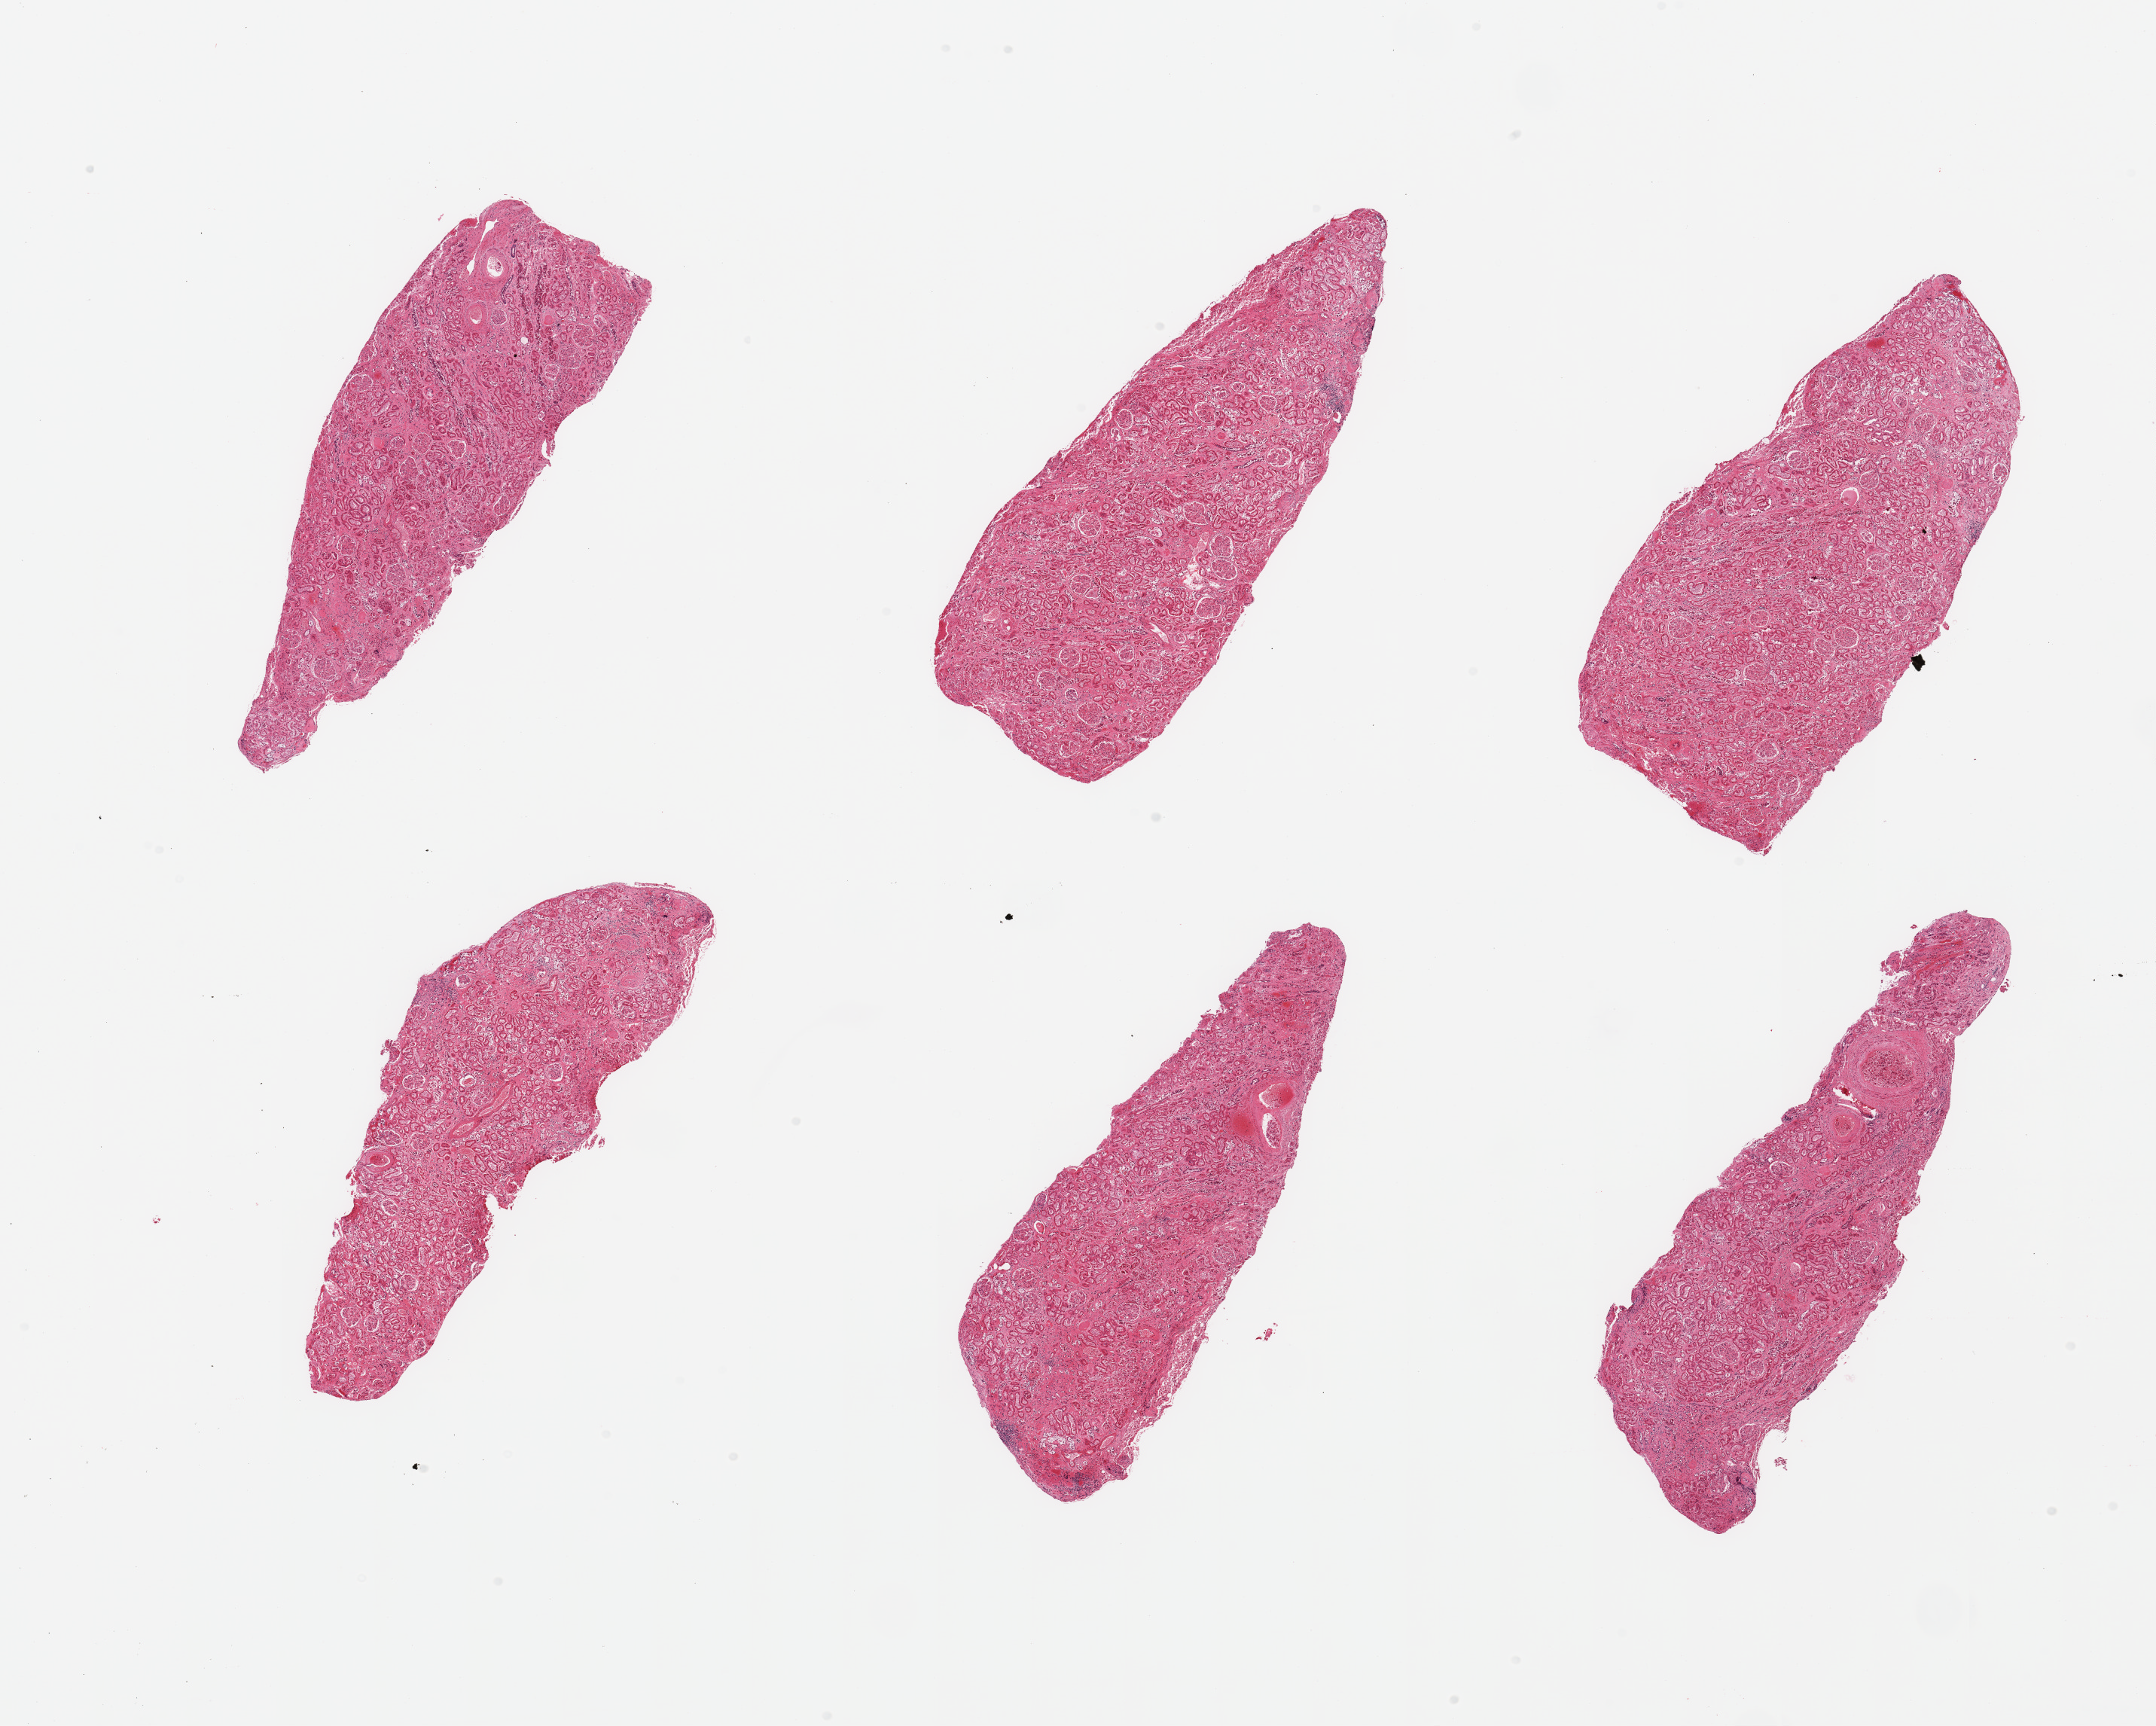
Digitized H&E-stained section — low-resolution overview of the scanned area, about 22.6 x 18.1 mm. PAXgene-fixed paraffin-embedded (PFPE) section. Target tissue: renal cortex. Donor tissue sample. Male donor.
• pathologist's review note for this sample: 6 pieces; arterial nephrosclerosis with moderate scarring